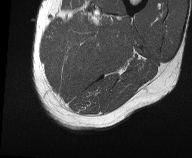
MRI of an extremity soft-tissue mass, one axial slice; slice 9 of 61 in the series (ordered by position); MR volume resampled by the dataset authors to the PET/CT grid (not the native acquisition matrix); 192 × 158 image matrix. Male patient. From the clinical record (not read from this slice): histological type: pleiomorphic liposarcoma; grade: high; site of the primary tumour: left thigh.
Structures marked on this image (expert contour drawn on MRI and transferred to this co-registered scan by the dataset authors):
- gross tumour volume including surrounding oedema: bounding box (x1, y1, x2, y2) in pixels: (70, 12, 113, 45)